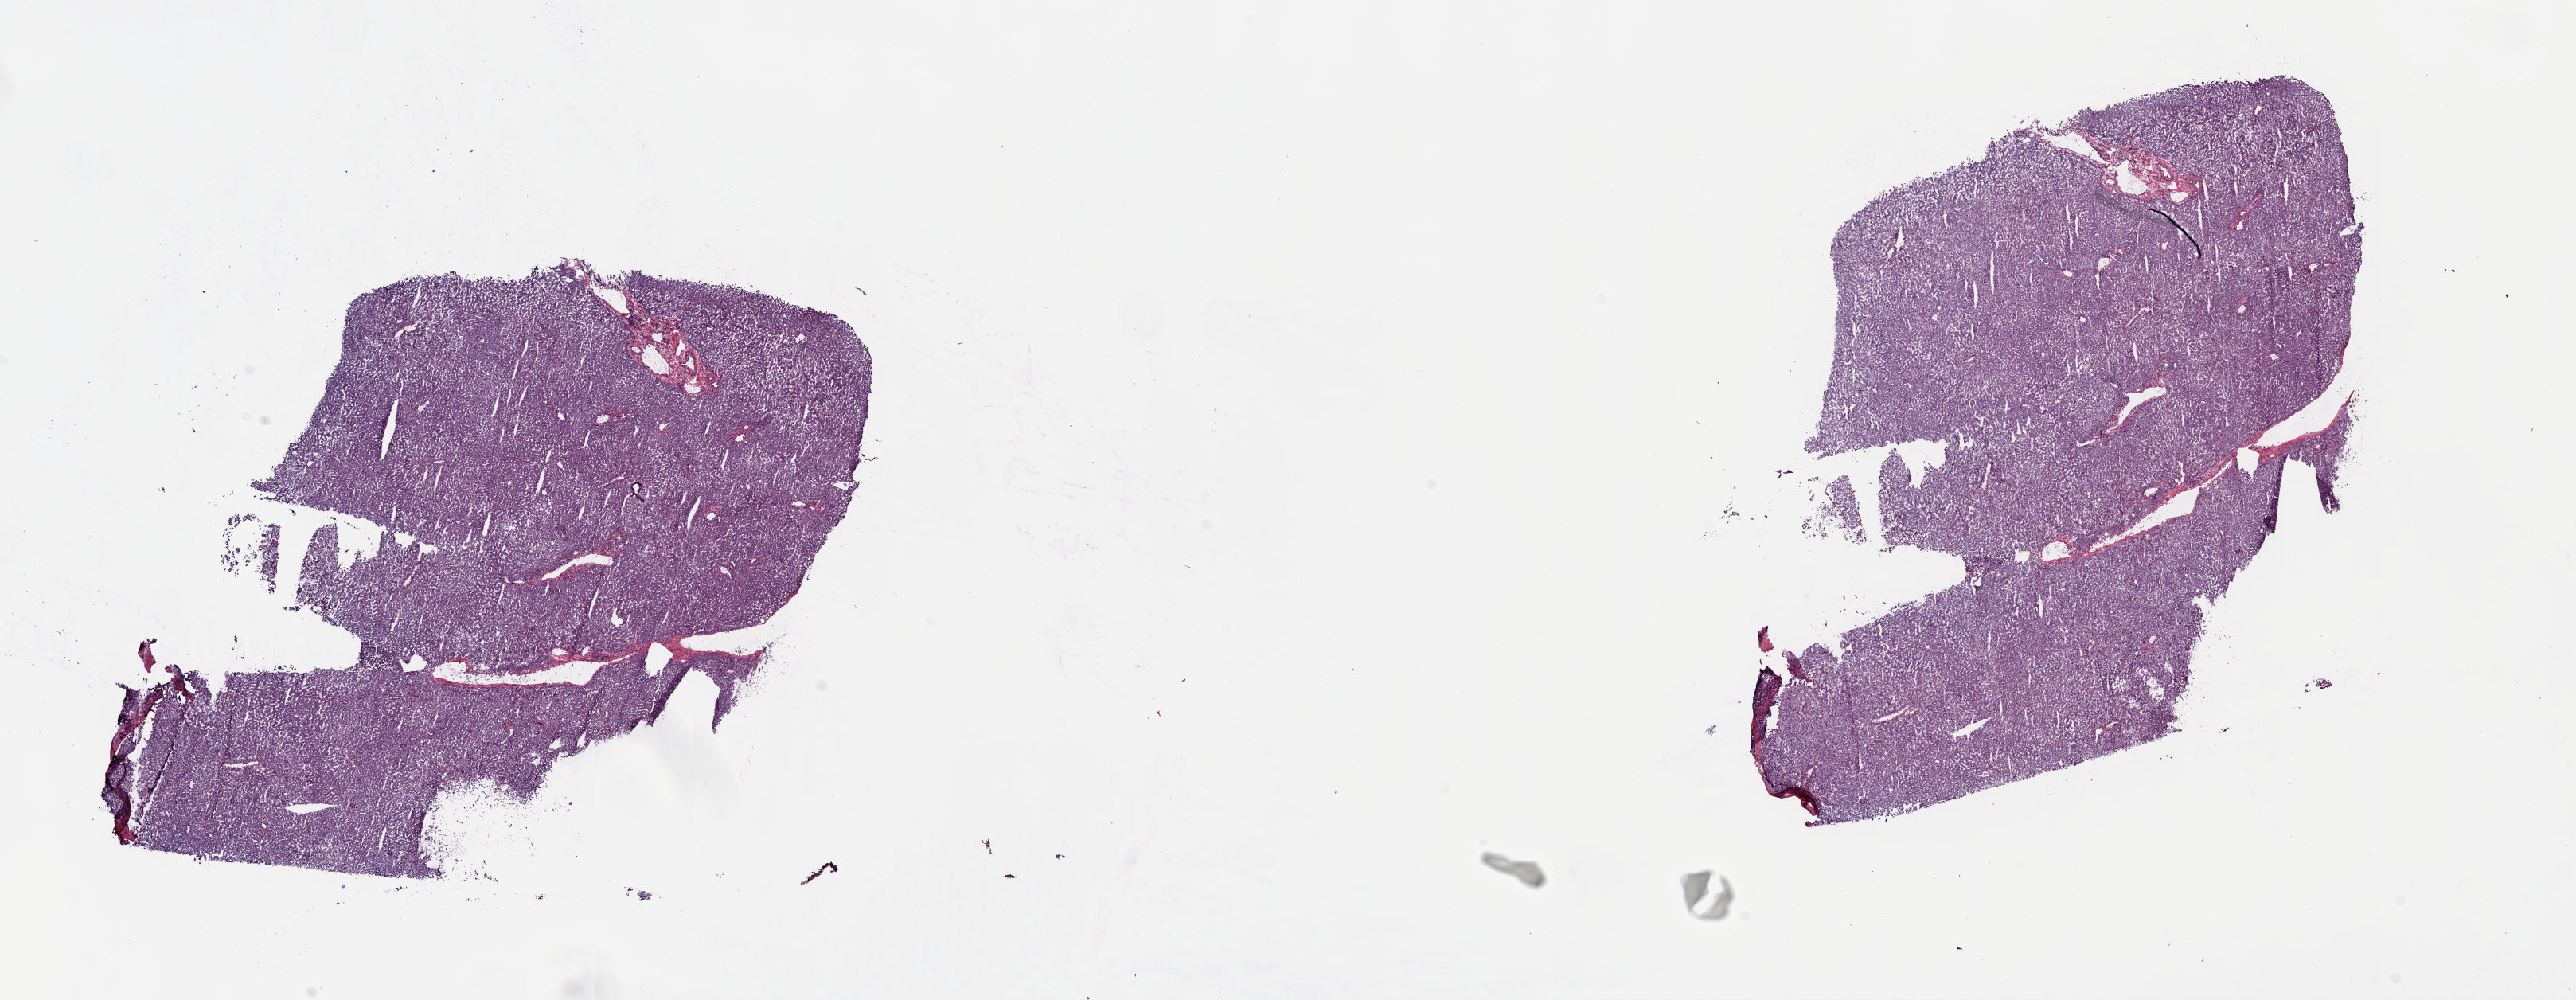
H&E-stained whole-slide image — whole scanned area (about 25.5 x 9.9 mm, from a 20x scan) shown as a low-resolution overview. Frozen section. Sample: solid tissue normal (non-tumour tissue), liver. Male patient; age at initial diagnosis 65 years. Slide review estimates, as recorded: tumour cells 0%, tumour nuclei 0%, normal cells 100%, stromal cells 0%, necrosis 0%. Inflammatory infiltration, as recorded: lymphocyte infiltration 5%, monocyte infiltration 0%, neutrophil infiltration 0%.
• this section: solid tissue normal sample (biorepository sample class)
• patient diagnosis: Hepatocellular carcinoma, NOS